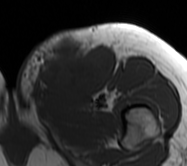
MRI of an extremity soft-tissue mass, one axial slice. Position 21 of 62 along the scan axis. MR volume resampled by the dataset authors to the PET/CT grid (not the native acquisition matrix). 3.27 mm slice thickness. 187 × 166 image matrix, field of view 183 × 162 mm. Female patient. Case-level facts recorded for this patient, not image findings: histological type: leiomyosarcoma; grade: high; site of the primary tumour: groin.
Structures marked on this image (expert contour drawn on MRI and transferred to this co-registered scan by the dataset authors):
- gross tumour volume including surrounding oedema: bounding box (x1, y1, x2, y2) in pixels: (16, 30, 115, 109)
- gross tumour volume (mass): (39, 42, 115, 100)